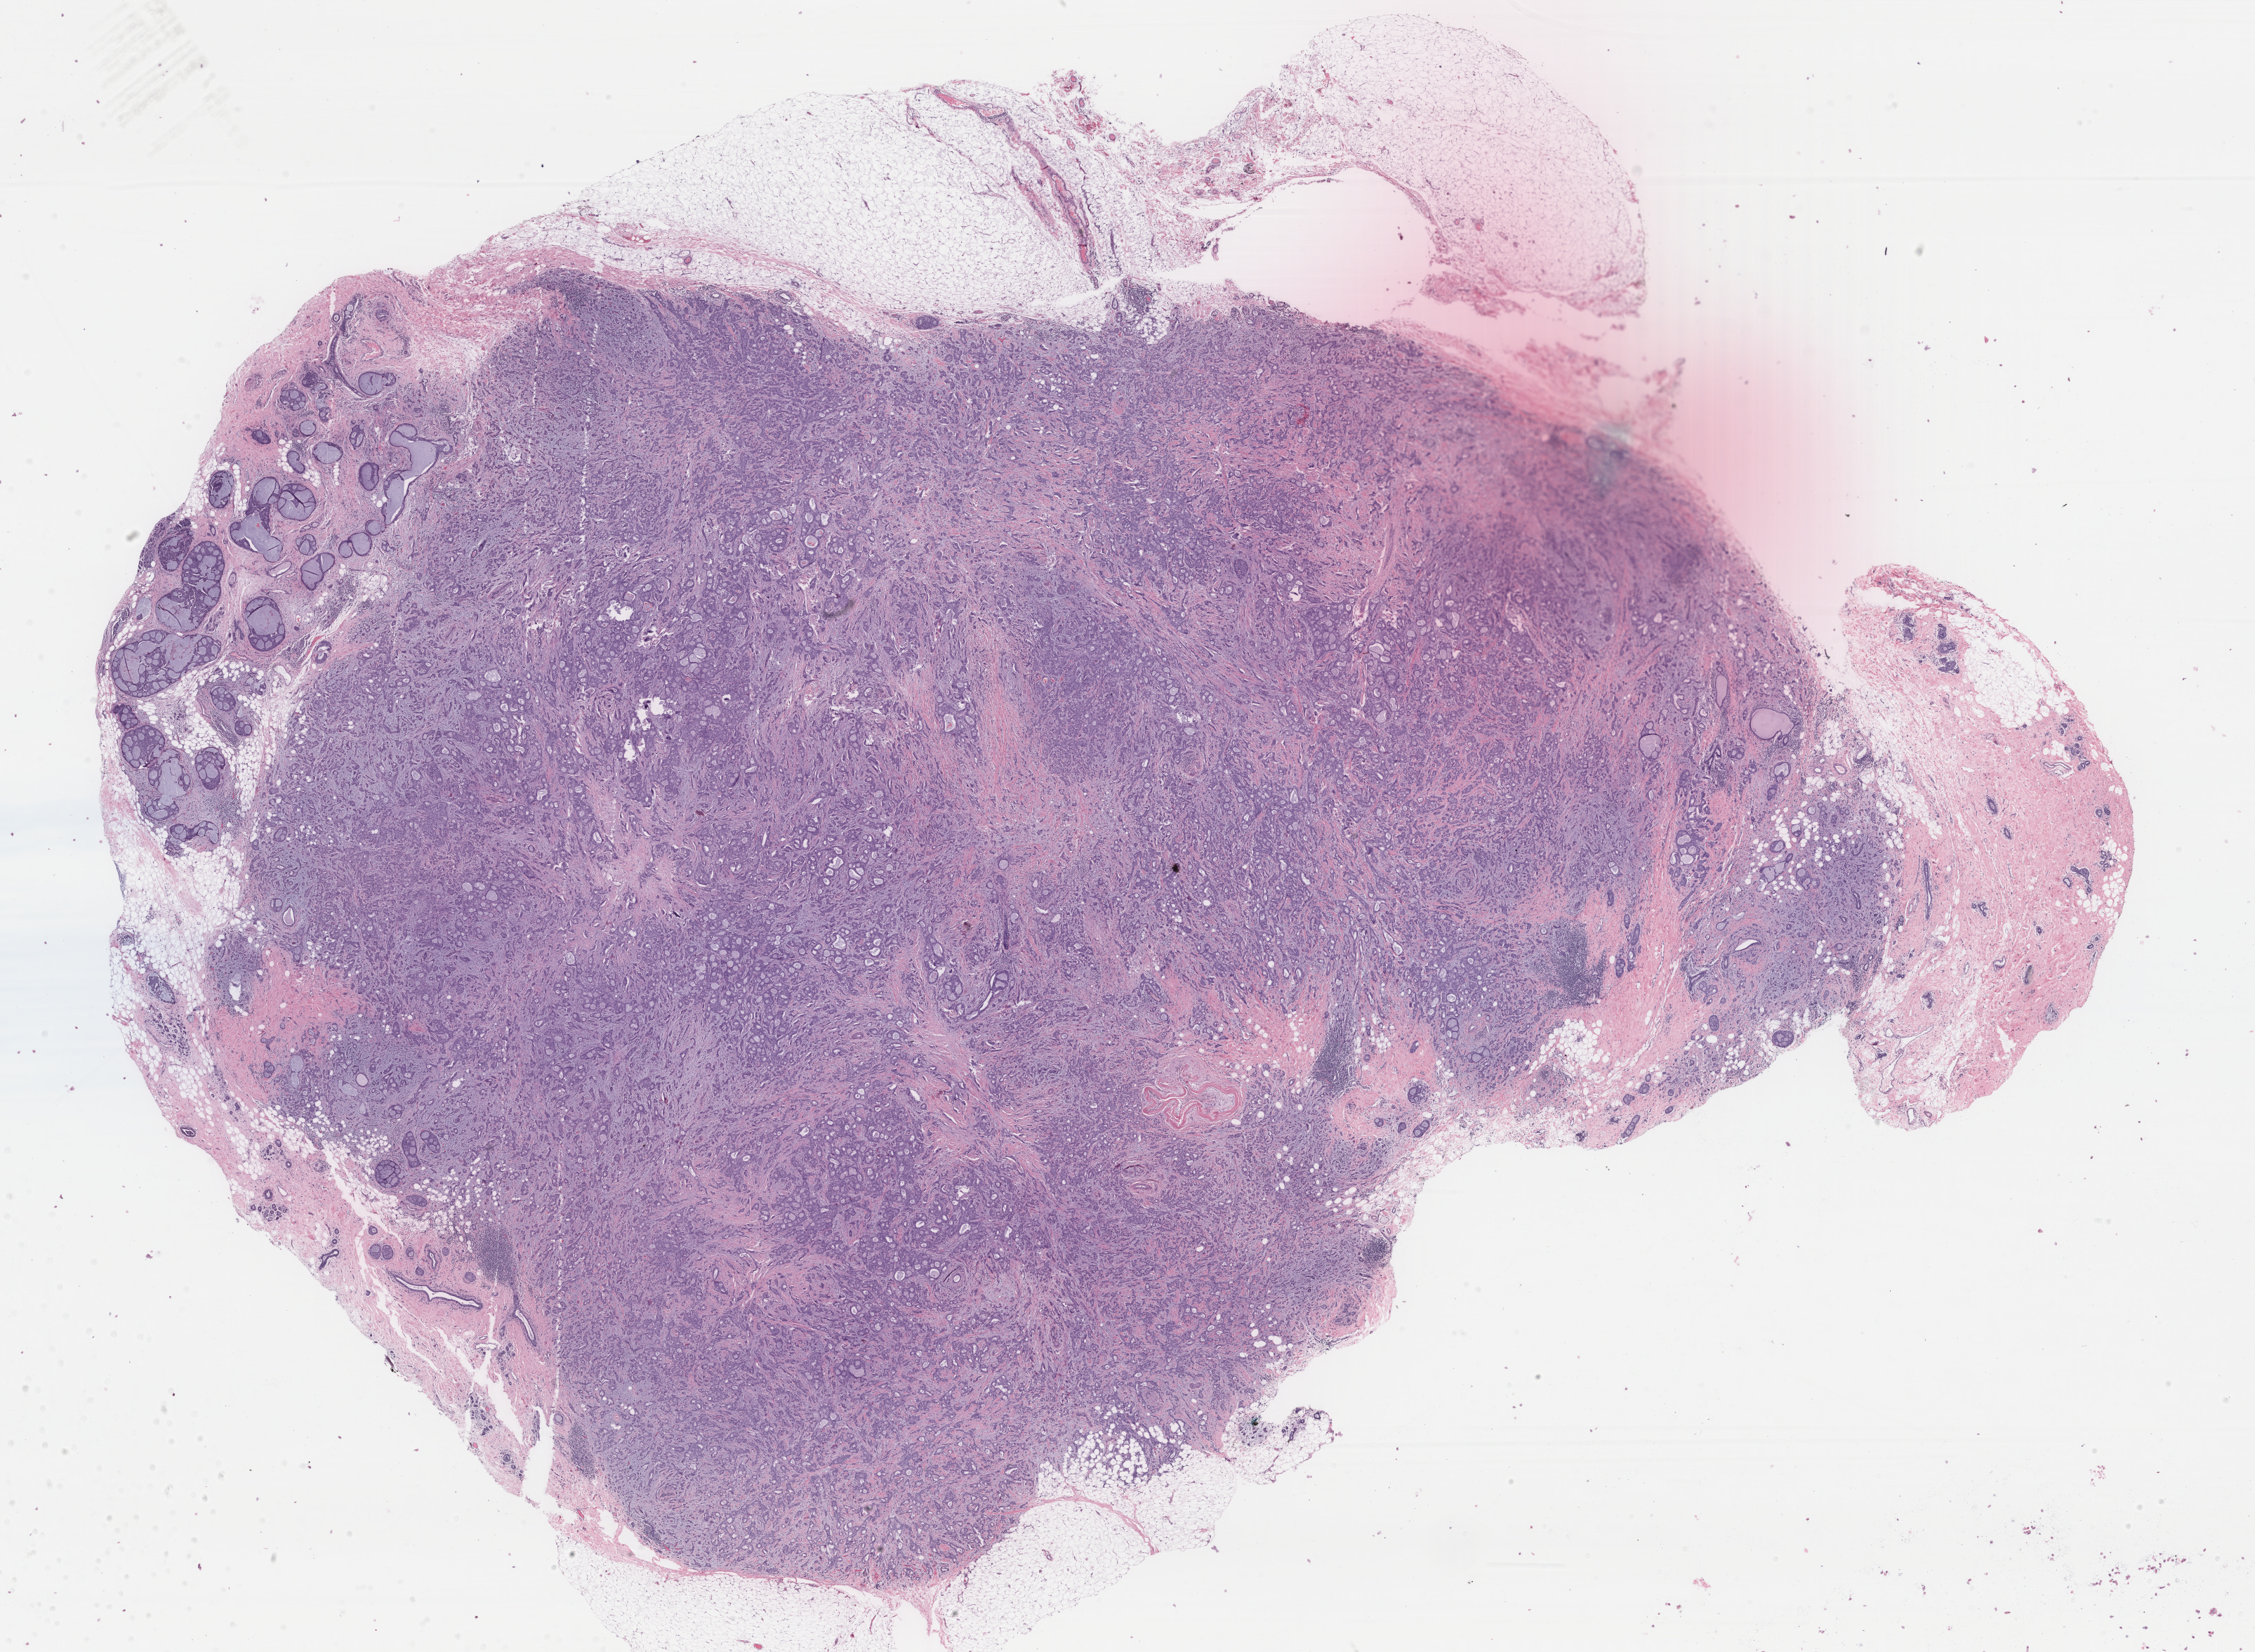
Digitized H&E tissue section (whole slide), a low-resolution overview of the entire scanned area, about 25.5 x 18.7 mm. Formalin-fixed paraffin-embedded (FFPE) diagnostic section. Primary tumour sample from the breast. Patient: female, age at initial diagnosis 50 years.
* pathologic diagnosis: Infiltrating duct carcinoma, NOS
* AJCC pathologic stage: IIB